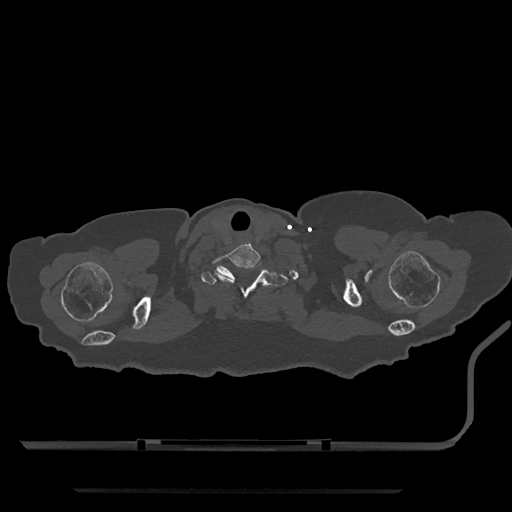
CT including the spine, one axial slice. Slice 723 of 797 in the series (ordered by position). 120 kVp. Bone window (W 1800 / L 400 HU). 512 × 512 image matrix. Female patient, age 51 years. From the clinical record (not read from this slice): primary cancer: neuro; vertebrae with lytic lesions (as recorded): T8.
Annotated regions visible in this slice (semi-automatic segmentation, software-assisted and operator-edited):
- T1 vertebra: bounding box <201,263,288,298> (left, top, right, bottom; pixels)